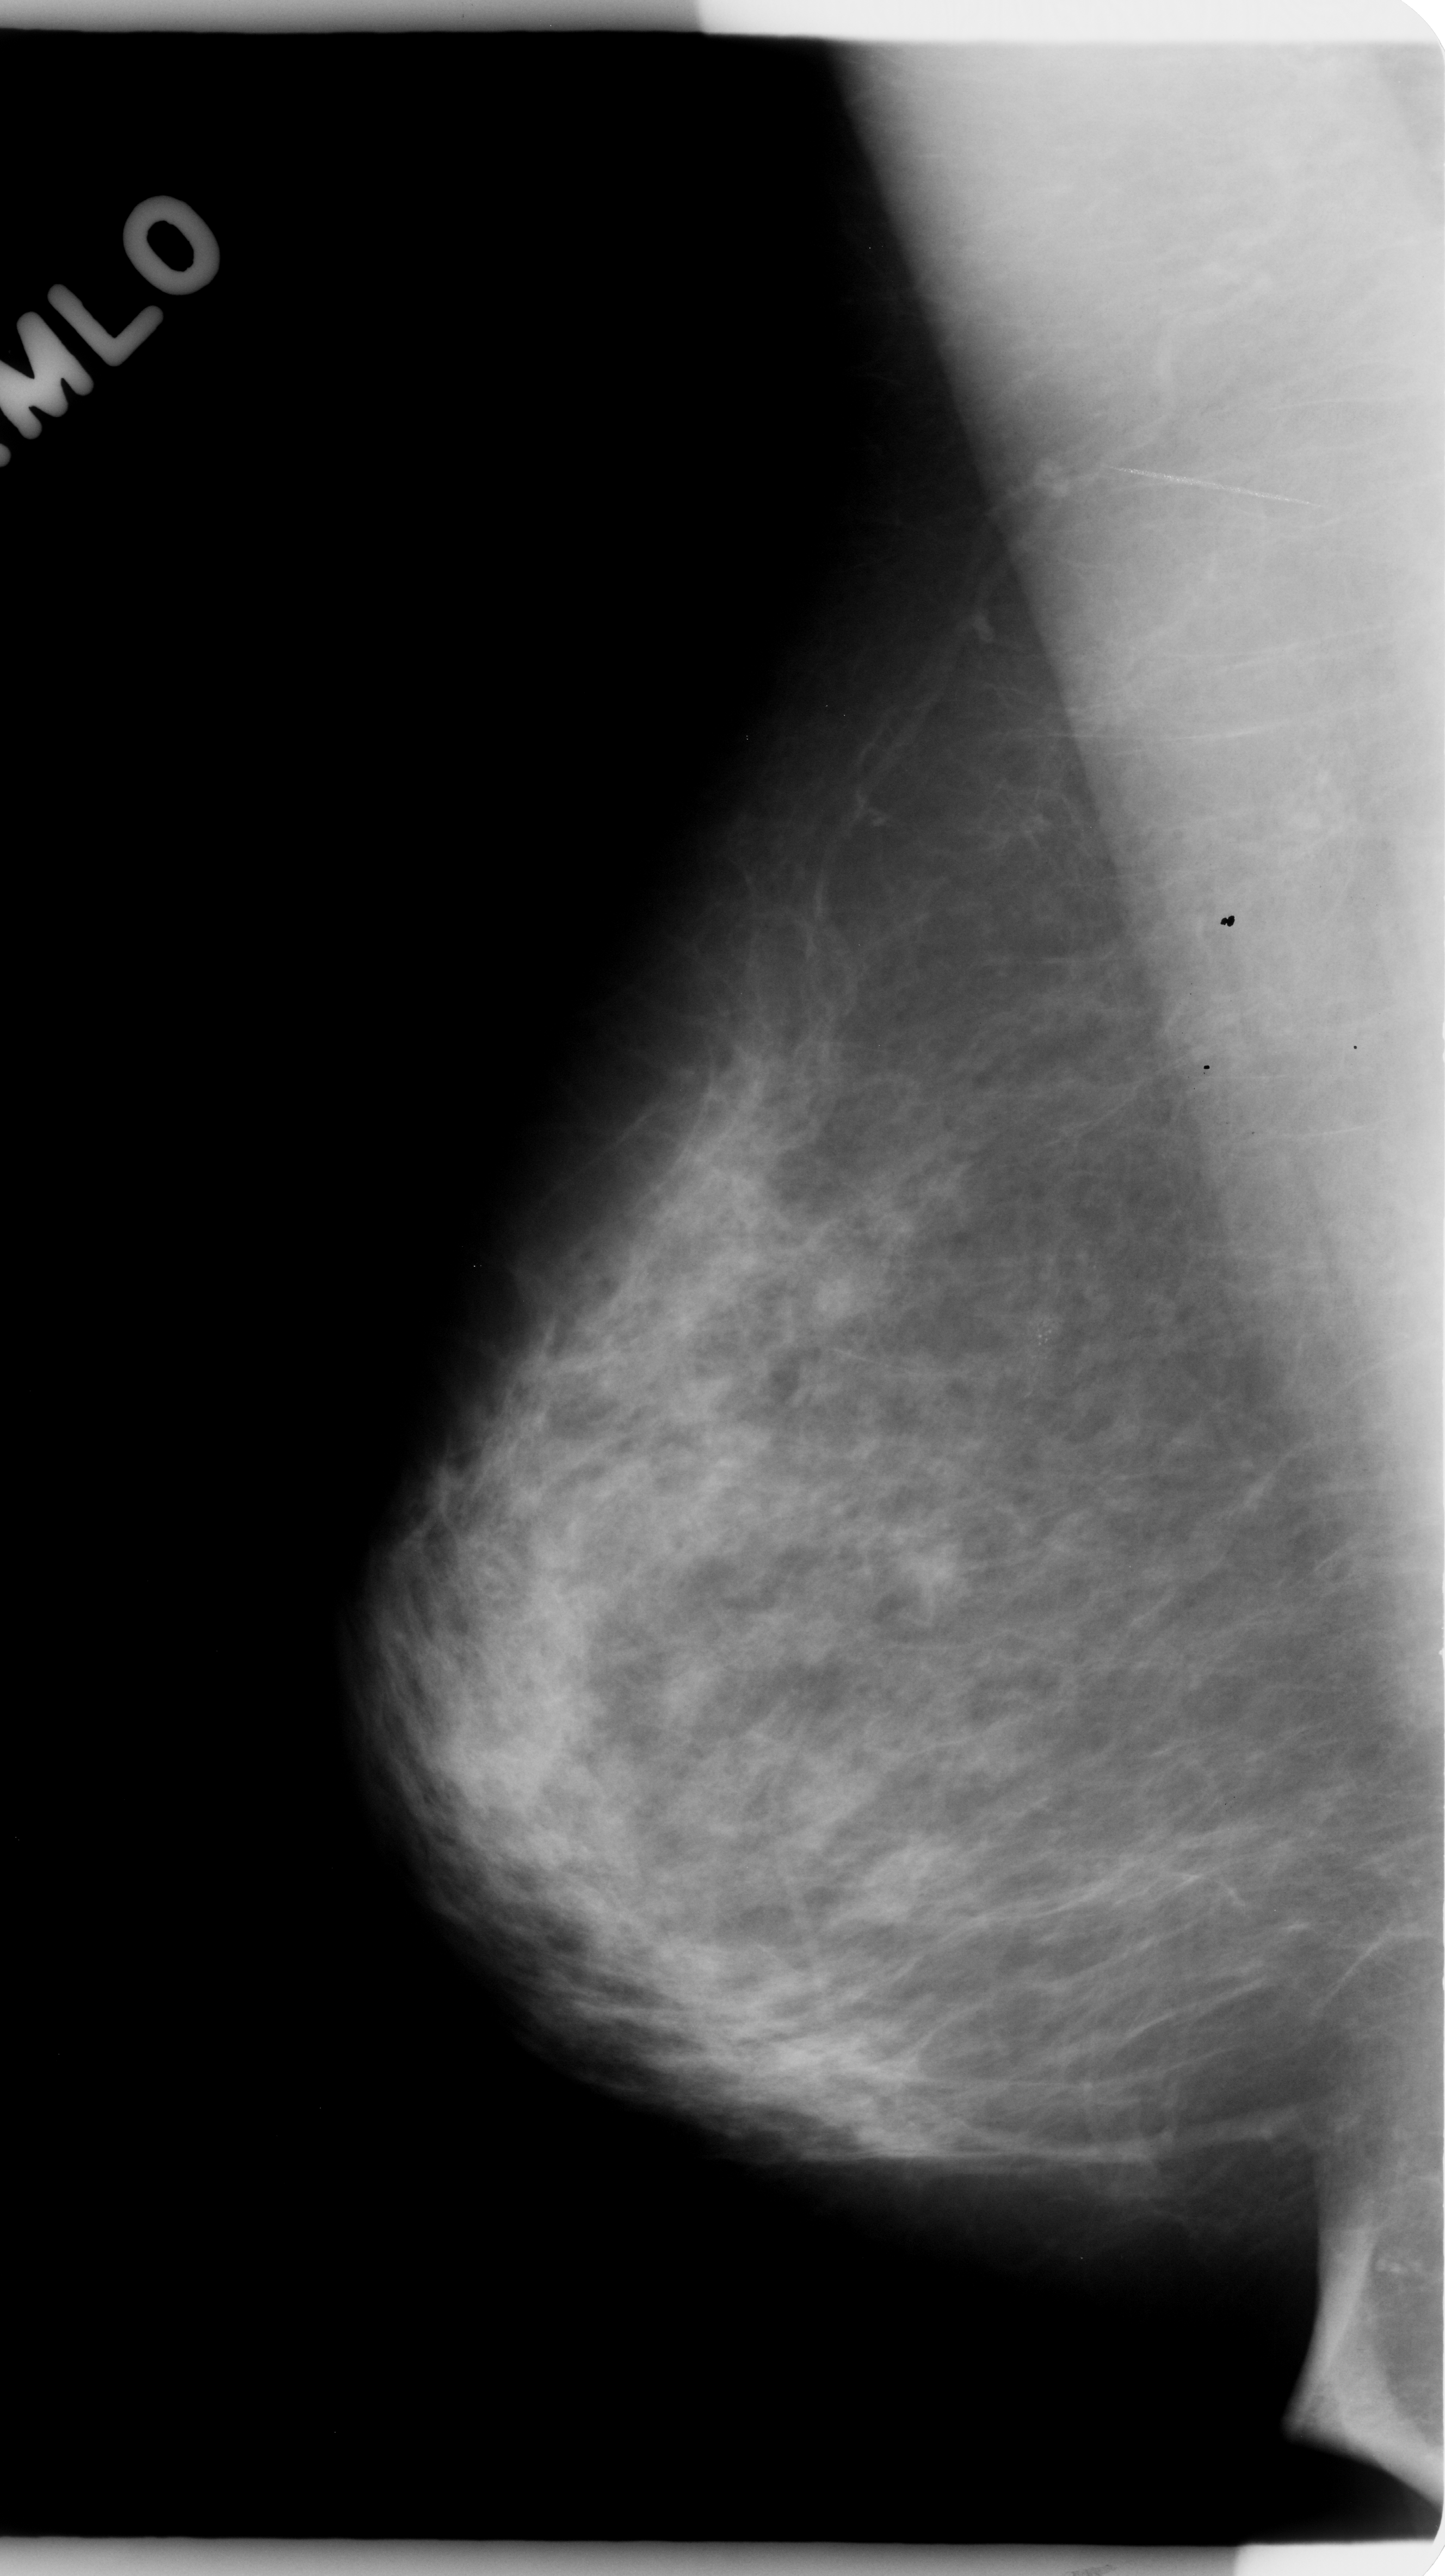
Mammogram (digitized film); right breast; MLO view; breast composition: scattered fibroglandular densities (BI-RADS density category 2 of 4).
Marked findings (only marked abnormalities are described; nothing is implied about the rest of the image): calcifications, morphology pleomorphic, distribution clustered; BI-RADS assessment category 4; pathology result (as recorded, not read from the image): malignant.